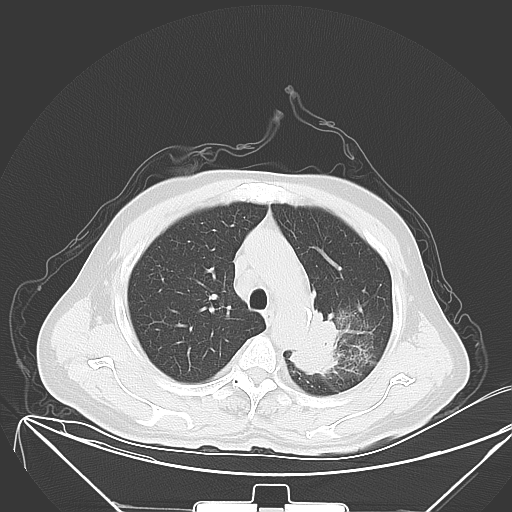
Chest CT, one axial slice; lung window (W 1500 / L -600 HU); 5 mm slice thickness; 512 × 512 image matrix. Patient: male, 58 years. Case-level facts recorded for this patient, not image findings: clinical TNM (as recorded): T2b N3 M1b; histopathological grade: G3.
Outlined on this slice (bounding box drawn by a radiologist):
- lung tumour (recorded histology: adenocarcinoma): bounding box <287,300,342,379> (left, top, right, bottom; pixels)